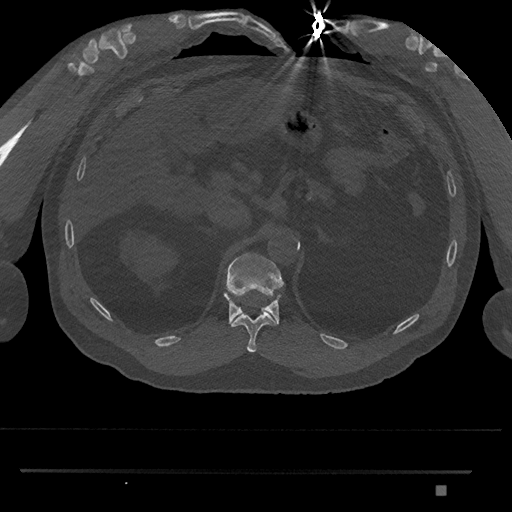
CT including the spine, one axial slice. Slice 919 of 1134 in the series (ordered by position). Reconstruction kernel Br40s/3. 120 kVp. Bone window (W 1800 / L 400 HU). 0.5 mm slice thickness. 512 × 512 image matrix, field of view 429 × 429 mm. Male patient, age 65 years. Case-level facts recorded for this patient, not image findings: primary cancer: prostate.
Outlined on this slice (semi-automatically segmented with operator editing):
- T11 vertebra: bounding box [x1, y1, x2, y2] px = [231, 312, 277, 353]
- T12 vertebra: [223, 252, 284, 325]